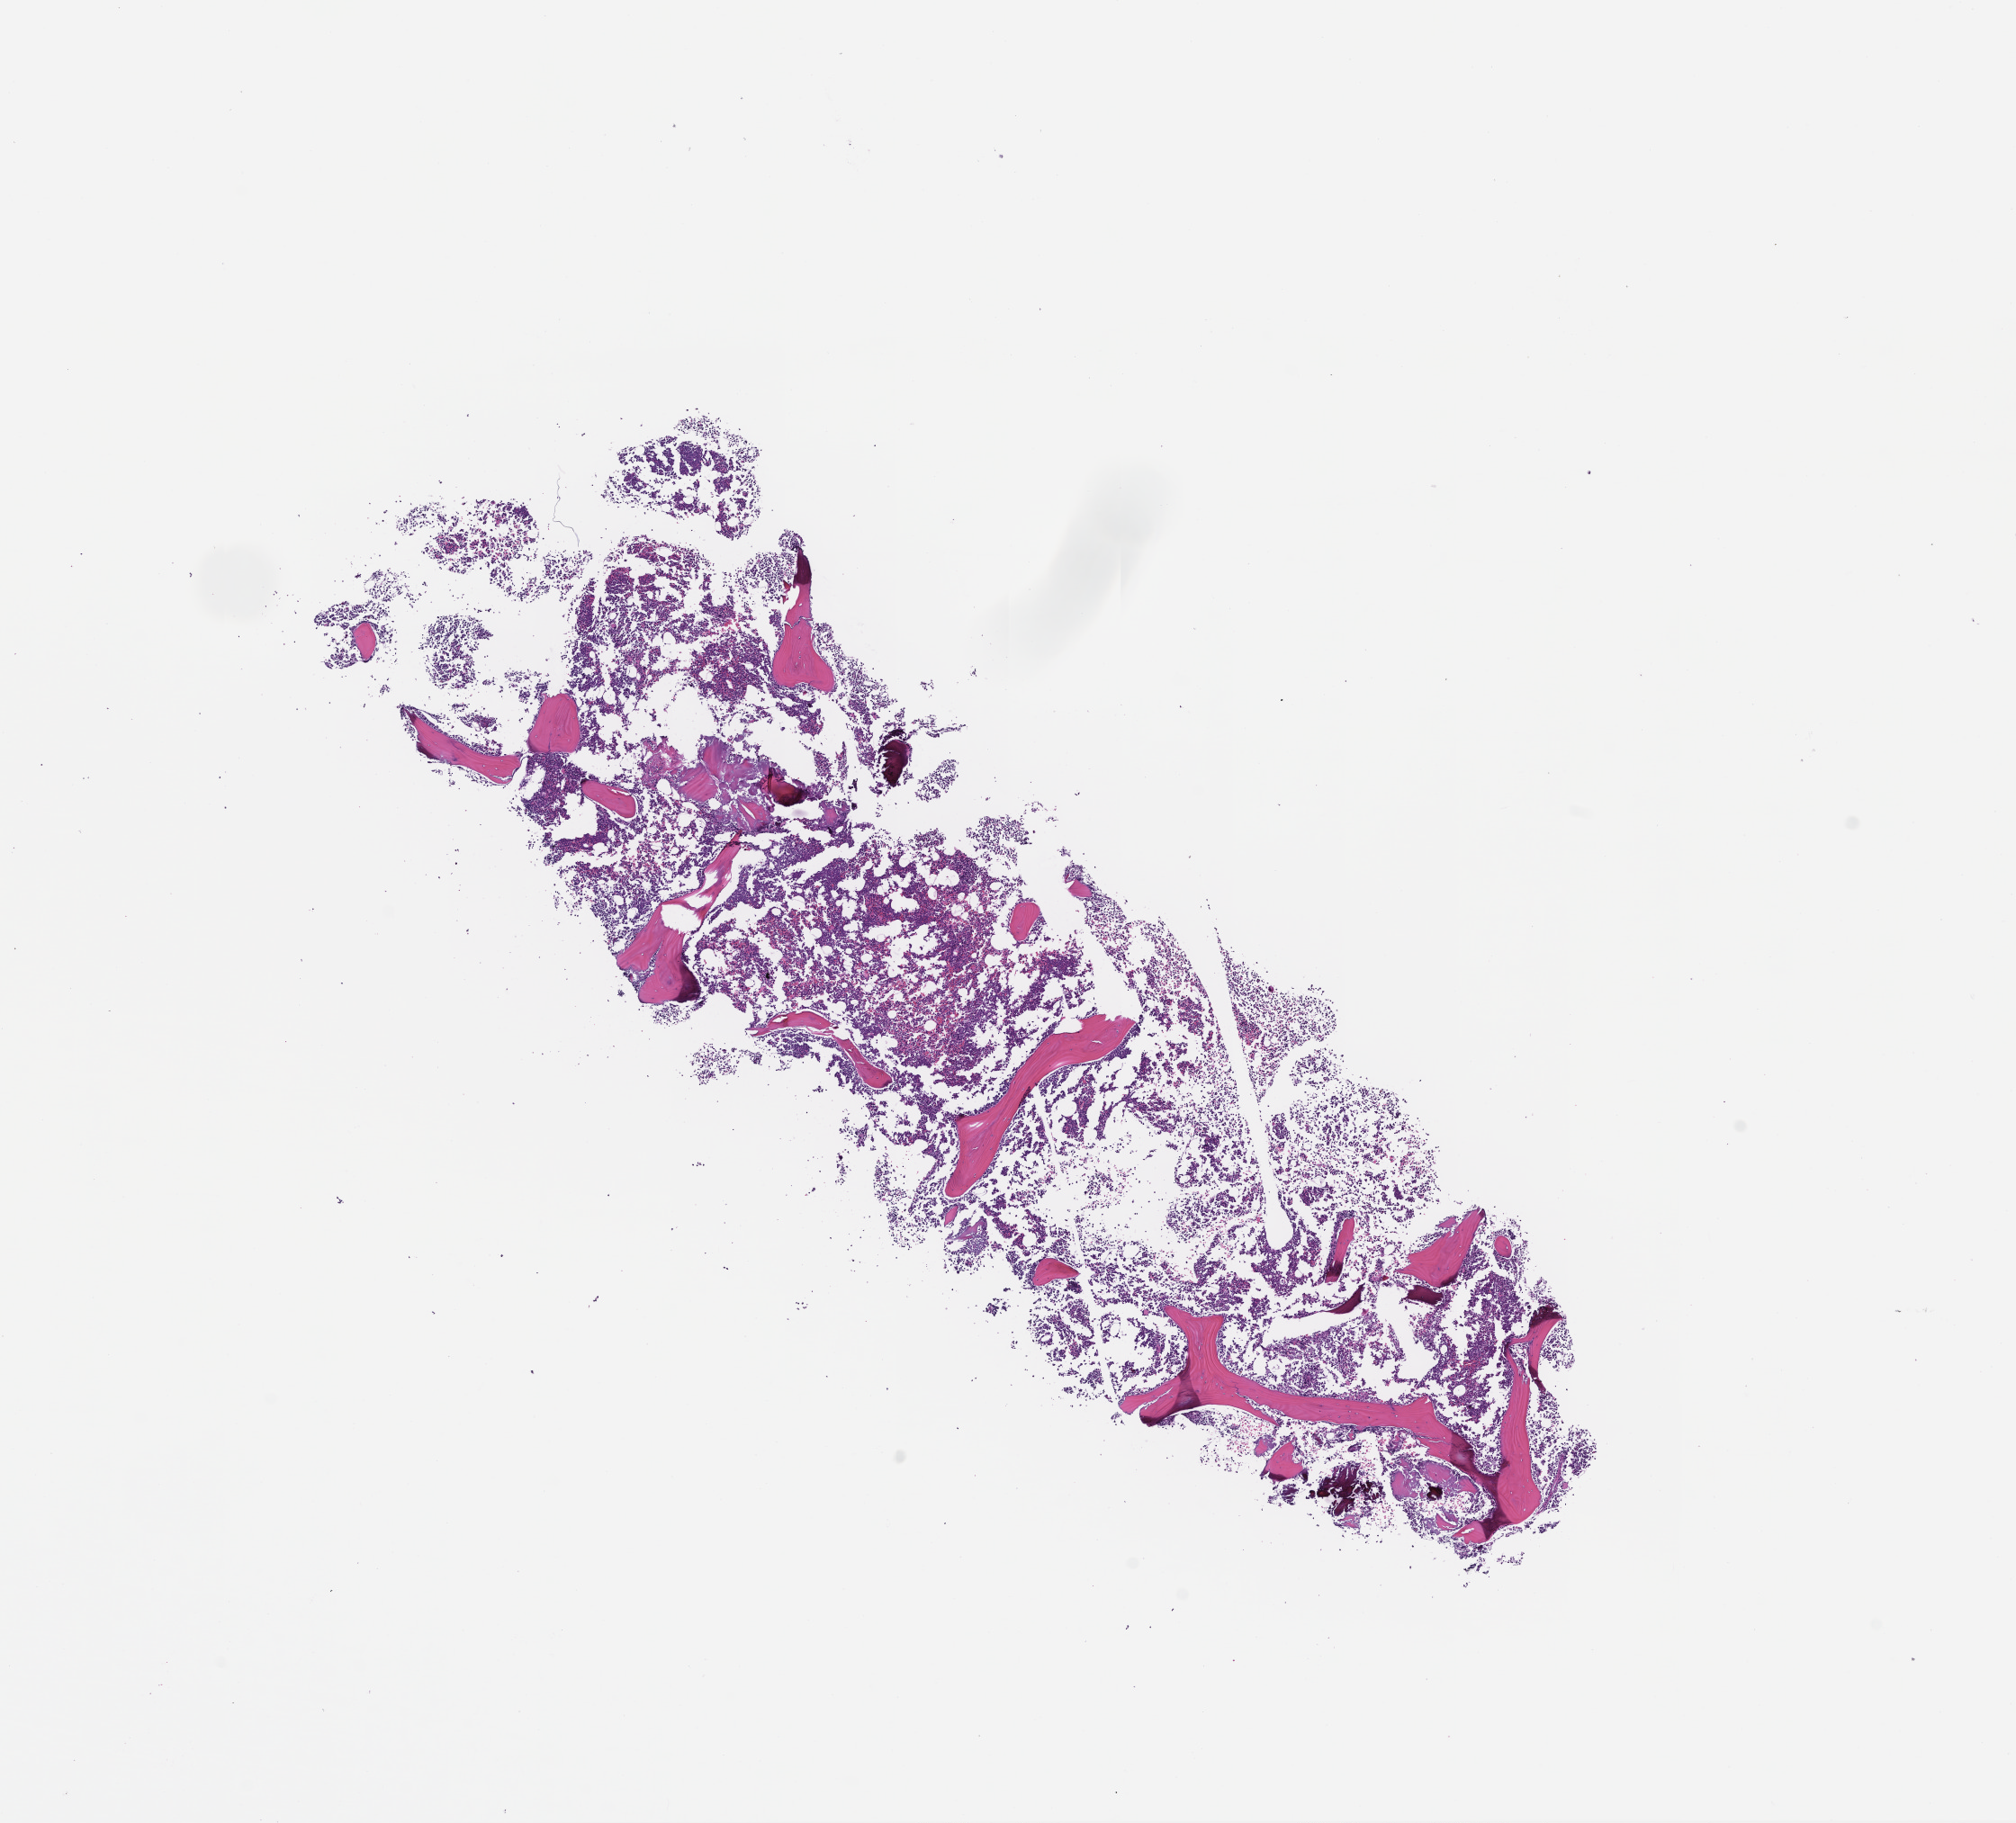
Digitized hematoxylin and eosin (H&E)-stained section — a low-resolution overview of the entire scanned area, about 9.0 x 8.2 mm; formalin-fixed, paraffin-embedded (FFPE) tissue; tissue site: bone marrow. Patient sex: male.
This section: primary tumour tissue. Diagnosis: Acute Myeloid Leukemia Not Otherwise Specified.